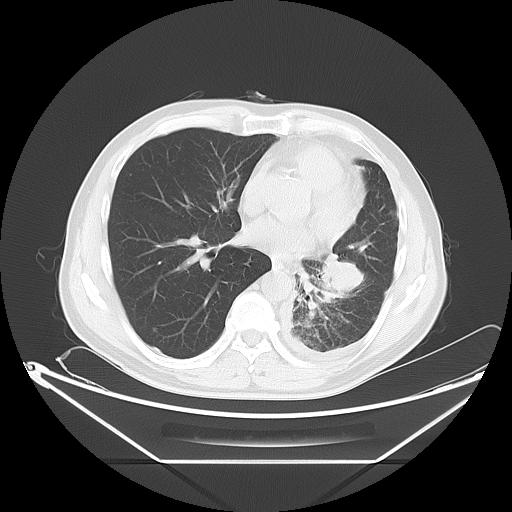
Chest CT, one axial slice; lung window (W 1500 / L -600 HU); 5 mm slice thickness; 512 × 512 image matrix, field of view 442 × 442 mm. Male patient, age 60 years. Case-level facts recorded for this patient, not image findings: clinical TNM (as recorded): T4 N1 M1.
Structures marked on this image (rectangle marked by the reading radiologist):
- lung tumour (recorded histology: adenocarcinoma): bounding box (x1, y1, x2, y2) in pixels: (304, 247, 362, 304)